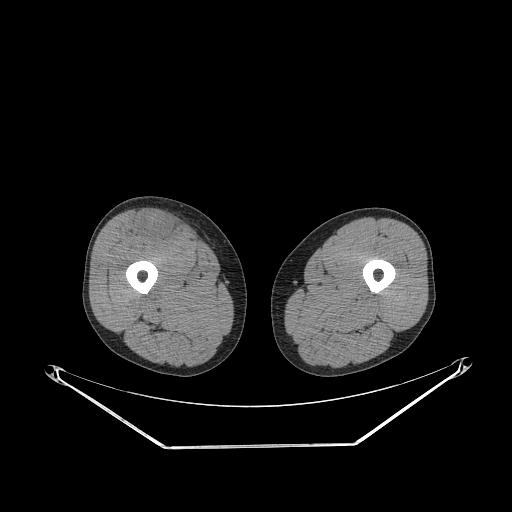
CT of an extremity soft-tissue mass (from a PET/CT study), one axial slice. Slice 256 of 311 in the series (ordered by position). Reconstruction kernel STANDARD. 140 kVp. Soft-tissue window (W 400 / L 40 HU). 3.75 mm slice thickness. 512 × 512 image matrix, field of view 500 × 500 mm. Male patient. From the clinical record (not read from this slice): histological type: pleiomorphic leiomyosarcoma; grade: intermediate; site of the primary tumour: right thigh.
Structures marked on this image (expert contour drawn on MRI and transferred to this co-registered scan by the dataset authors):
- gross tumour volume including surrounding oedema: box from (x=137, y=212) to (x=182, y=243) px